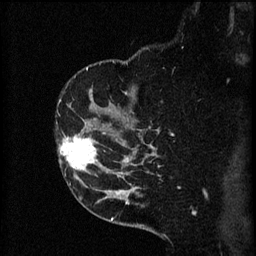
Breast MRI (dynamic contrast-enhanced), one sagittal slice. 3 images stored at this slice position (order not interpretable as contrast timing). 1.5 T. TE 4.2 ms, TR 8.2 ms. 2 mm slice thickness. 256 × 256 image matrix, field of view 180 × 180 mm. Female patient, age 49 years.
Annotated regions visible in this slice (semi-automatic segmentation, software-assisted and operator-edited):
- analysis volume of interest (the breast-tissue region the enhancement analysis was run in; not a lesion): bounding box [x1, y1, x2, y2] px = [57, 126, 105, 177]
- tumour enhancement mask (voxels above the 70 % enhancement threshold inside the analysis volume of interest): [59, 136, 105, 173]